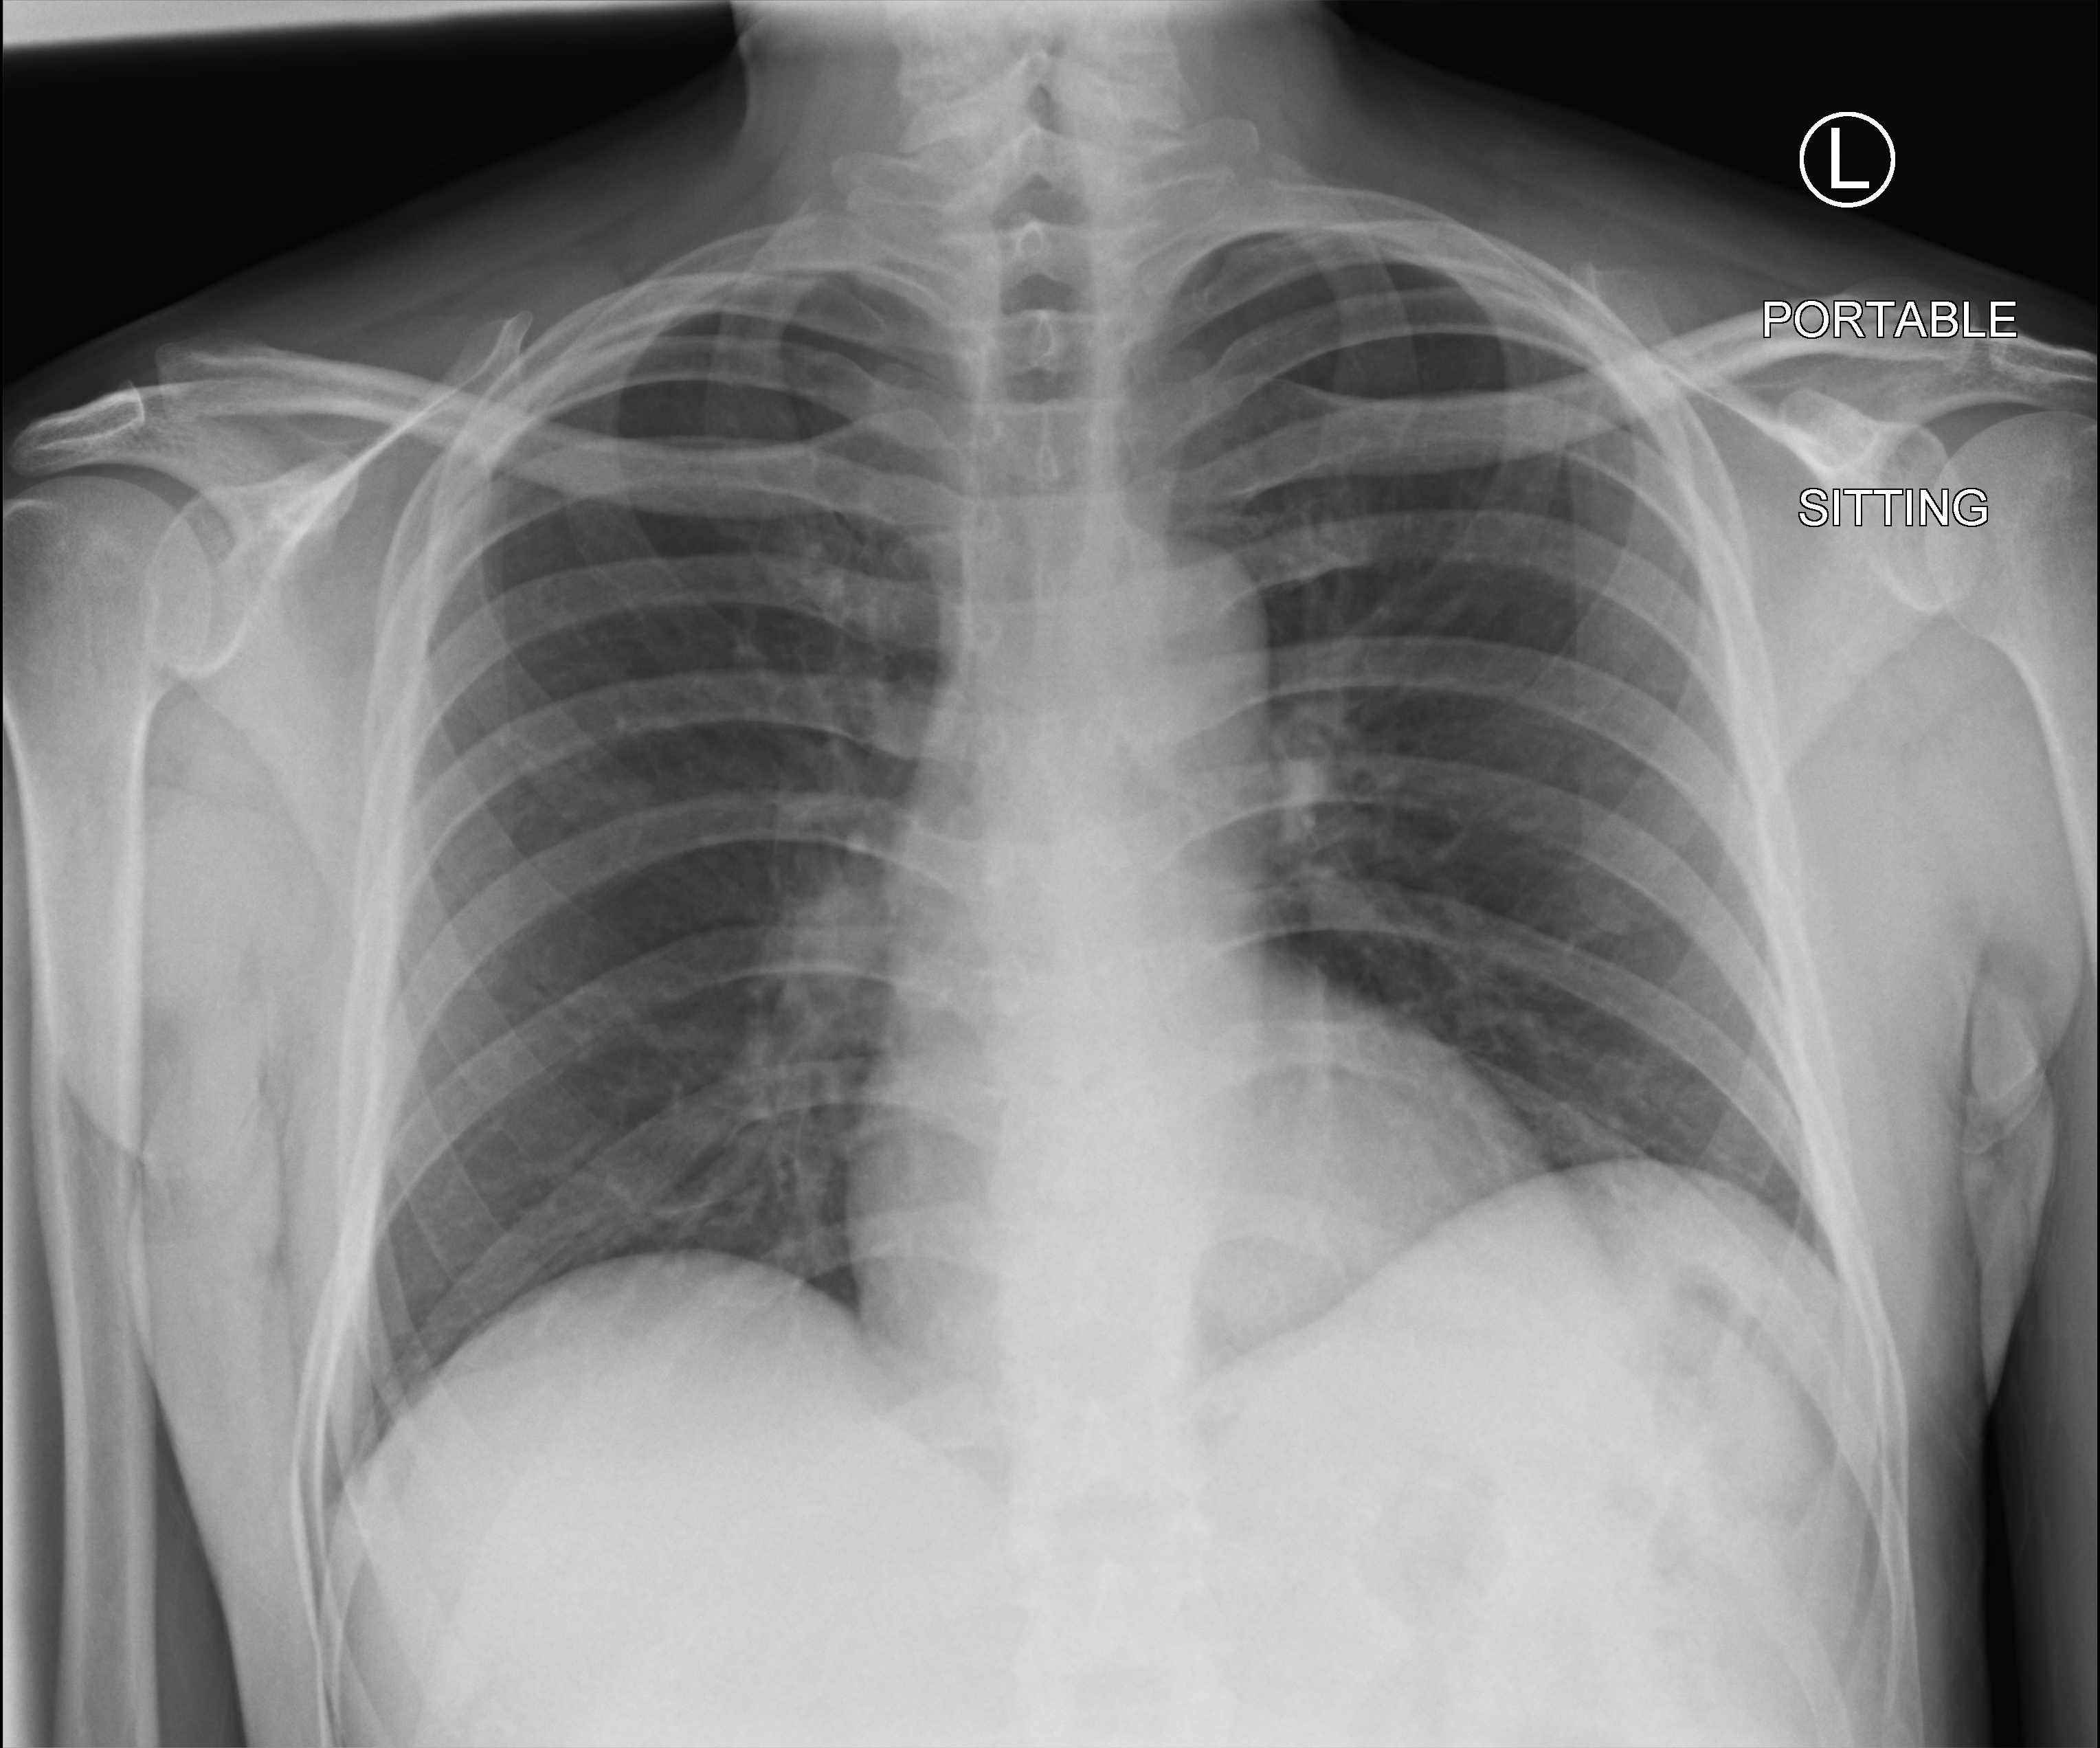
Portable chest radiograph; anteroposterior (AP) projection. Patient hospitalised with COVID-19; male, aged 18–59 years.
Hospital-stay facts (about this admission, not read from this image; timing relative to this image not recorded): mechanically ventilated during this hospital stay: no.